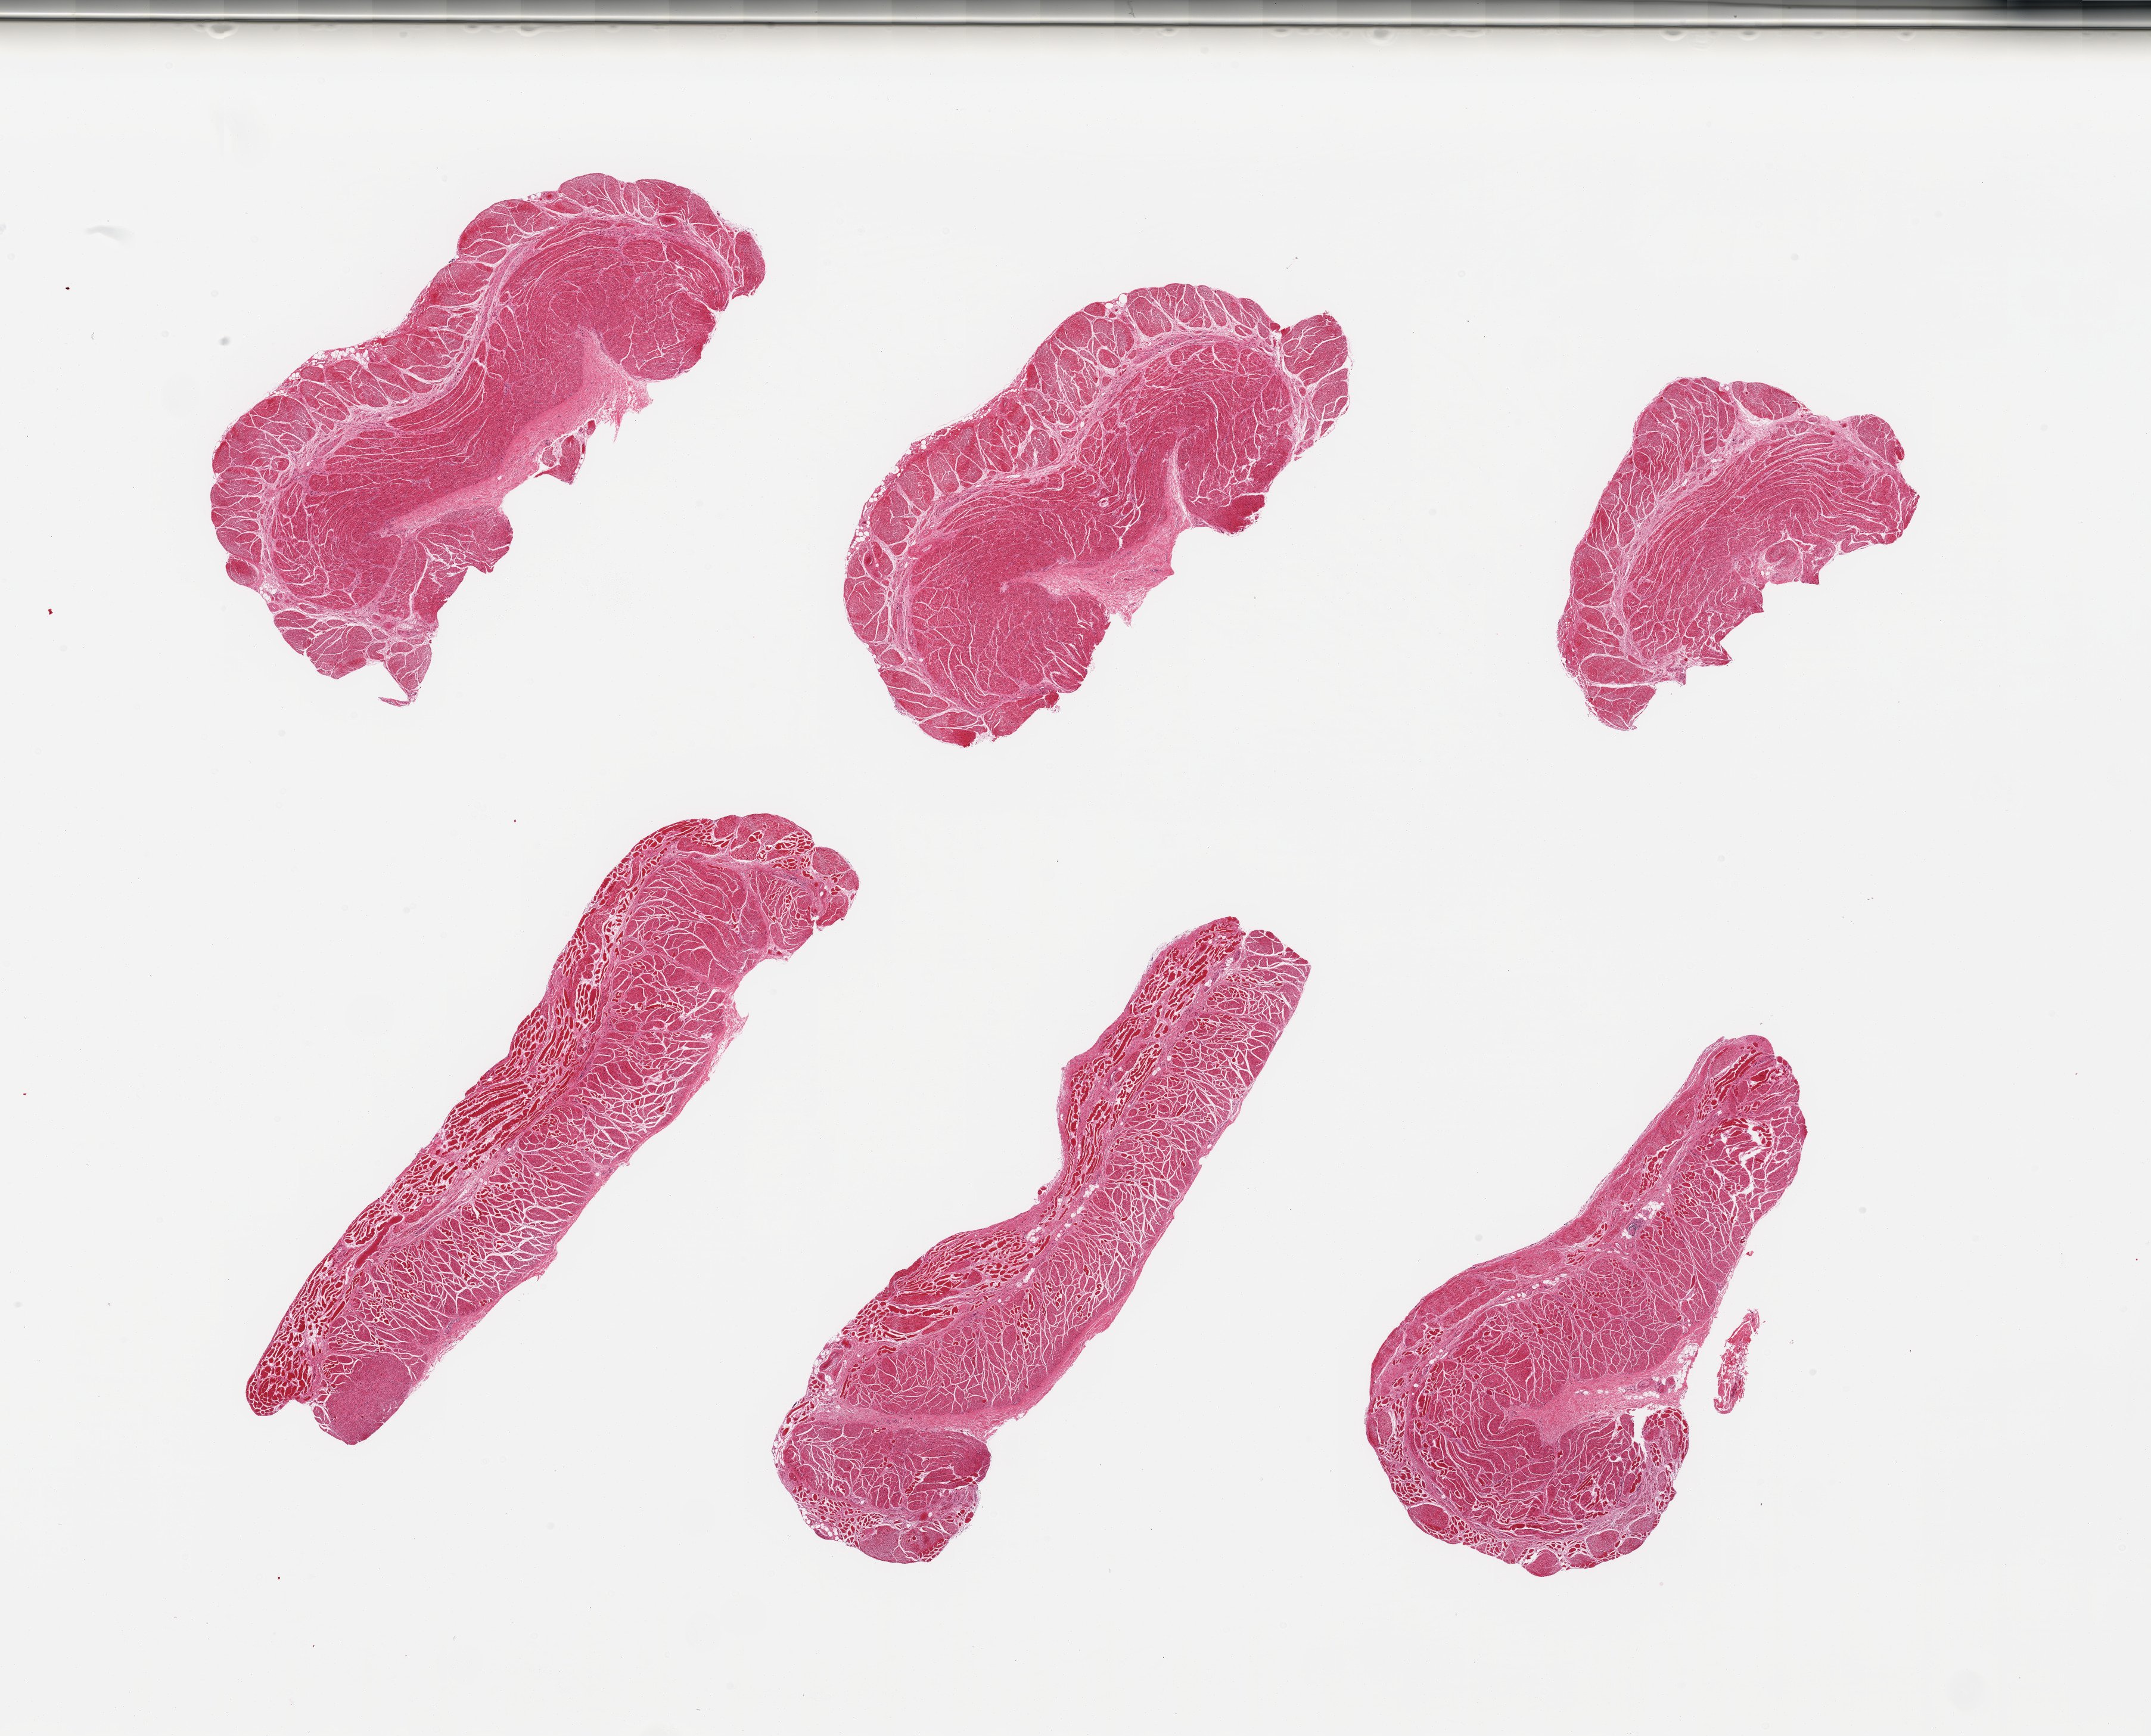
Whole-slide image, haematoxylin and eosin stain, whole scanned area (about 28.5 x 23.0 mm) shown as a low-resolution overview; PAXgene-fixed, paraffin-embedded tissue; sampled site (target tissue): esophageal muscle; donor tissue sample. Male donor.
Pathologist's review note for this sample: 6 pieces; well trimmed target muscularis.